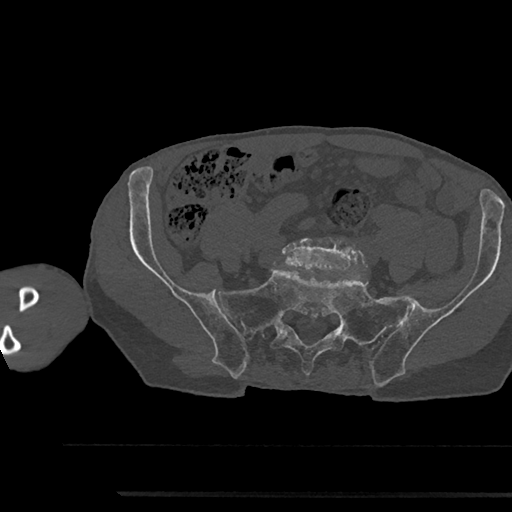
CT including the spine, one axial slice; slice 296 of 797 in the series (ordered by position); reconstruction kernel Br40s/3; bone window (W 1800 / L 400 HU); 0.5 mm slice thickness; 512 × 512 image matrix, field of view 367 × 367 mm. Male patient, age 79 years. From the clinical record (not read from this slice): primary cancer: prostate.
Annotated regions visible in this slice (semi-automatic segmentation, software-assisted and operator-edited):
- L5 vertebra: box from (x=281, y=237) to (x=367, y=272) px